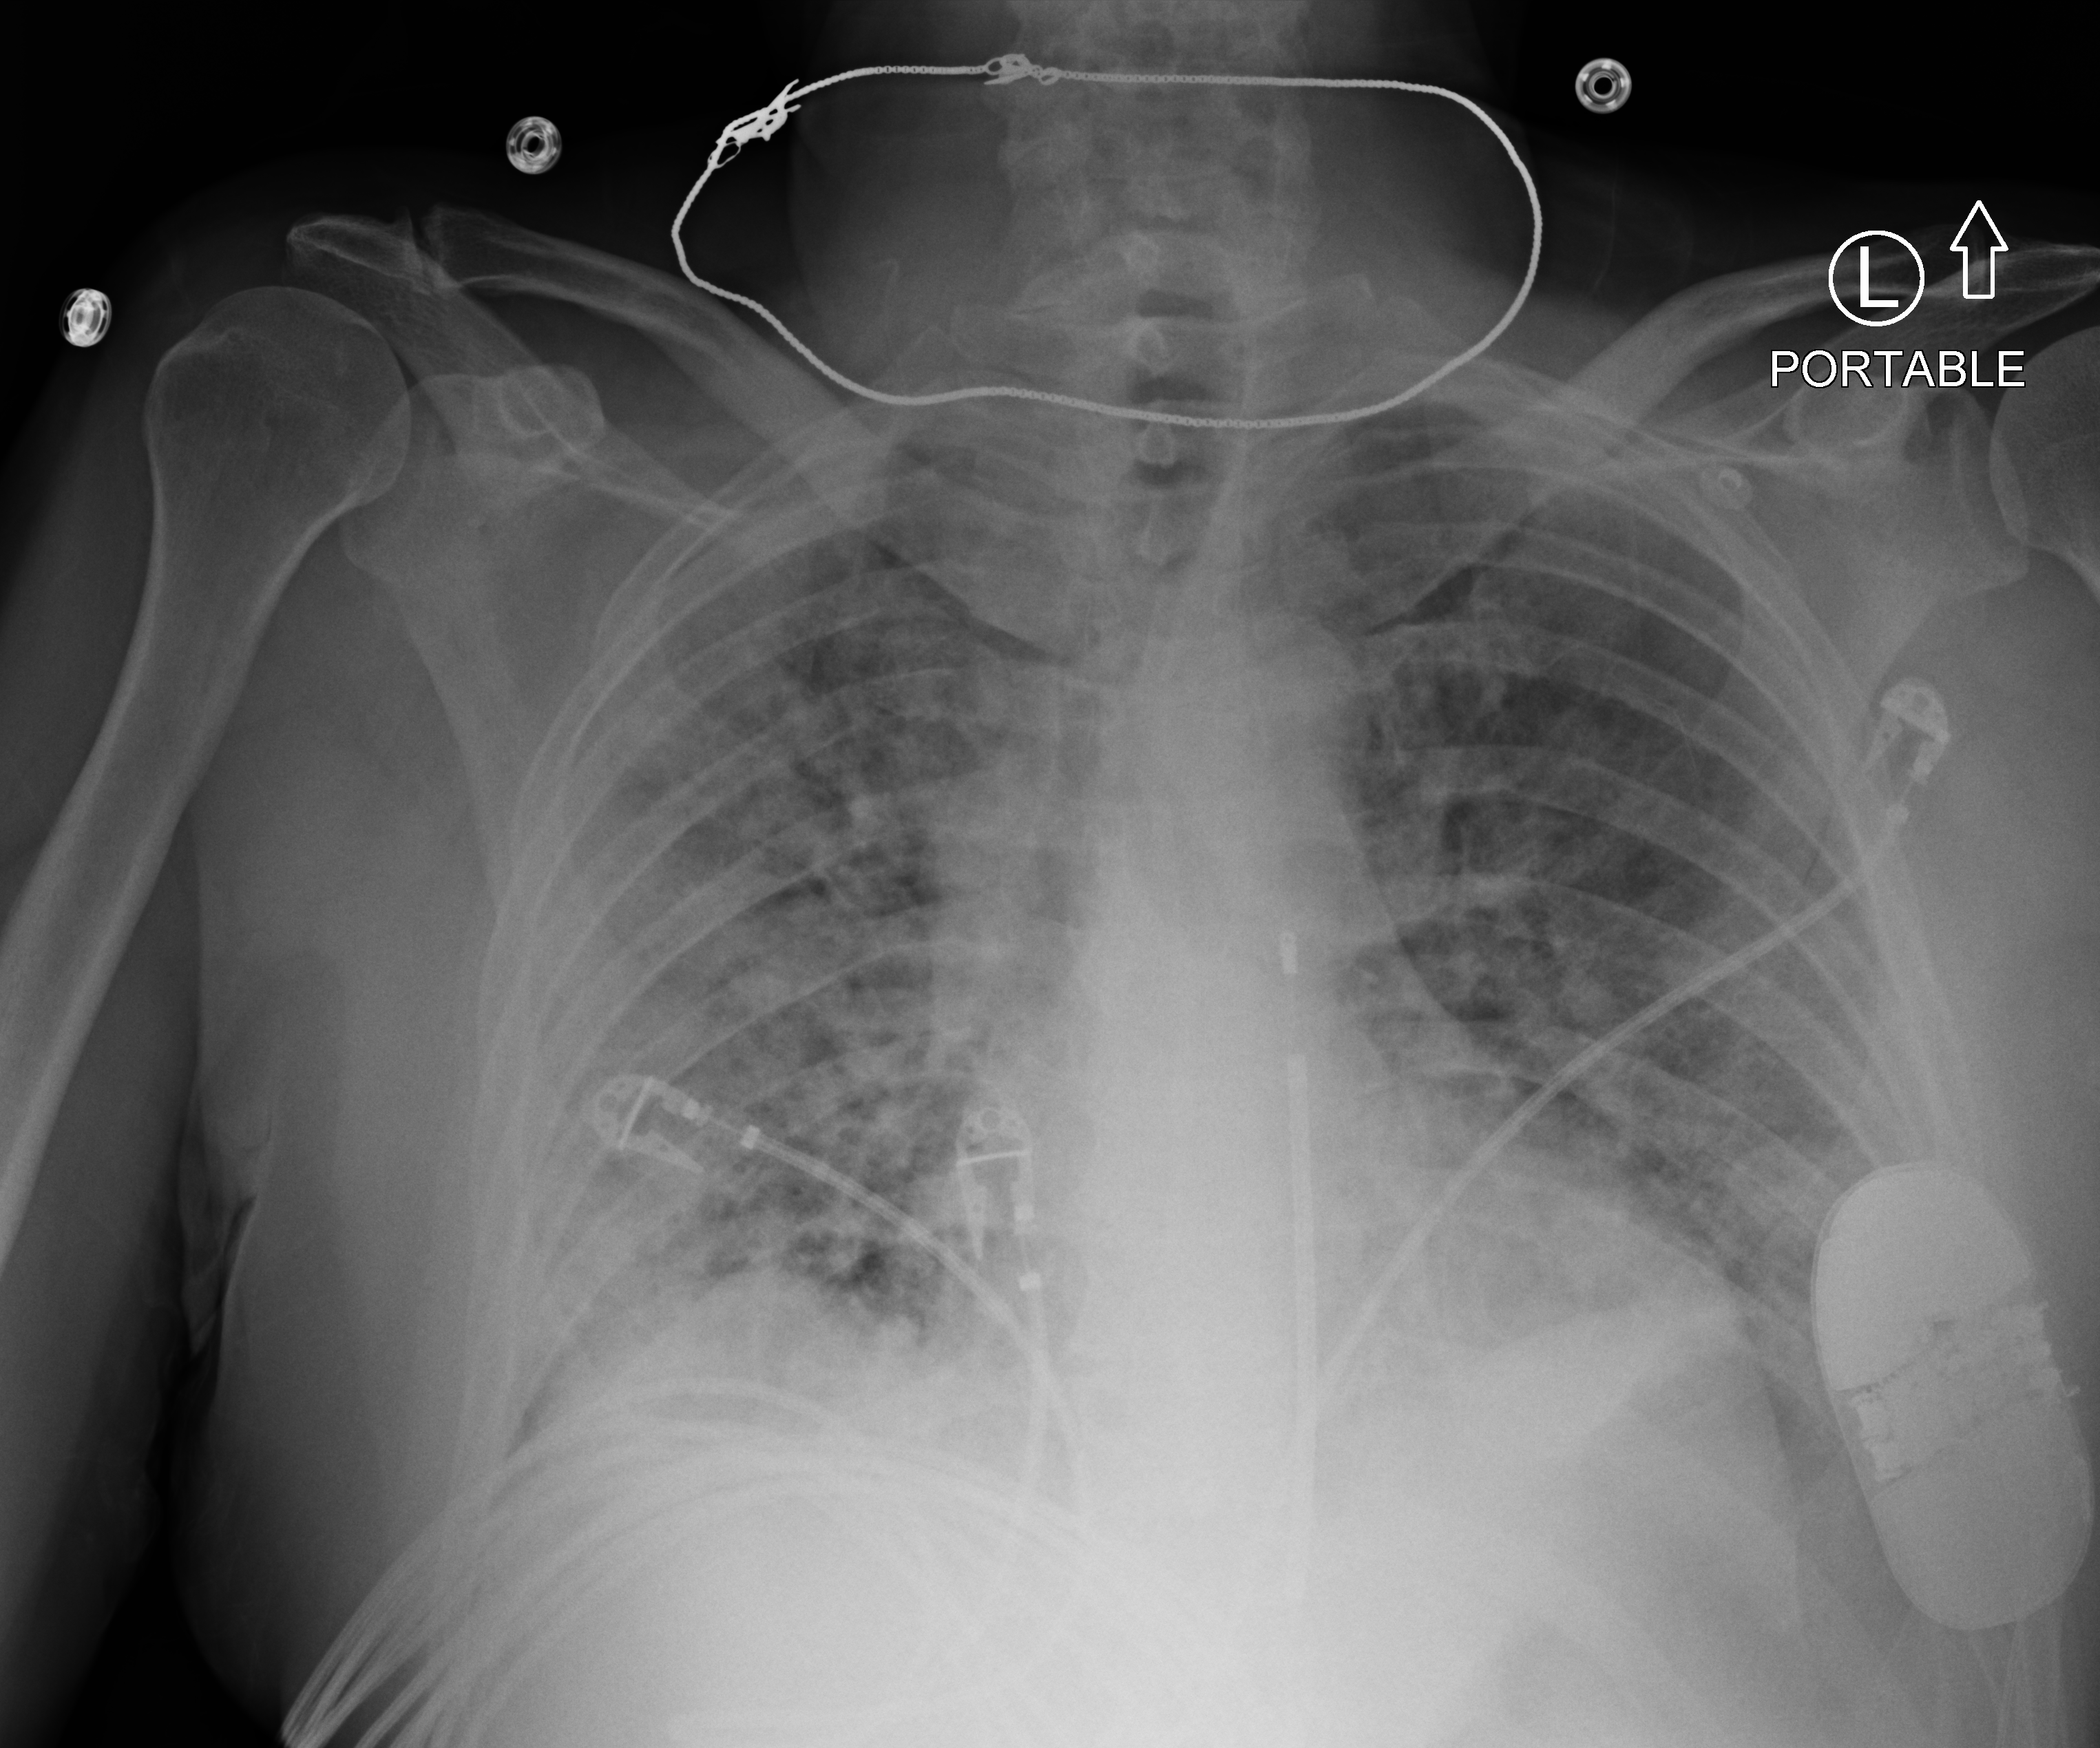
Chest X-ray (portable), anteroposterior (AP) projection. Male patient hospitalised with COVID-19, age 18–59 years.
Hospital-stay facts (about this admission, not read from this image; timing relative to this image not recorded): admitted to intensive care during this hospital stay: no.